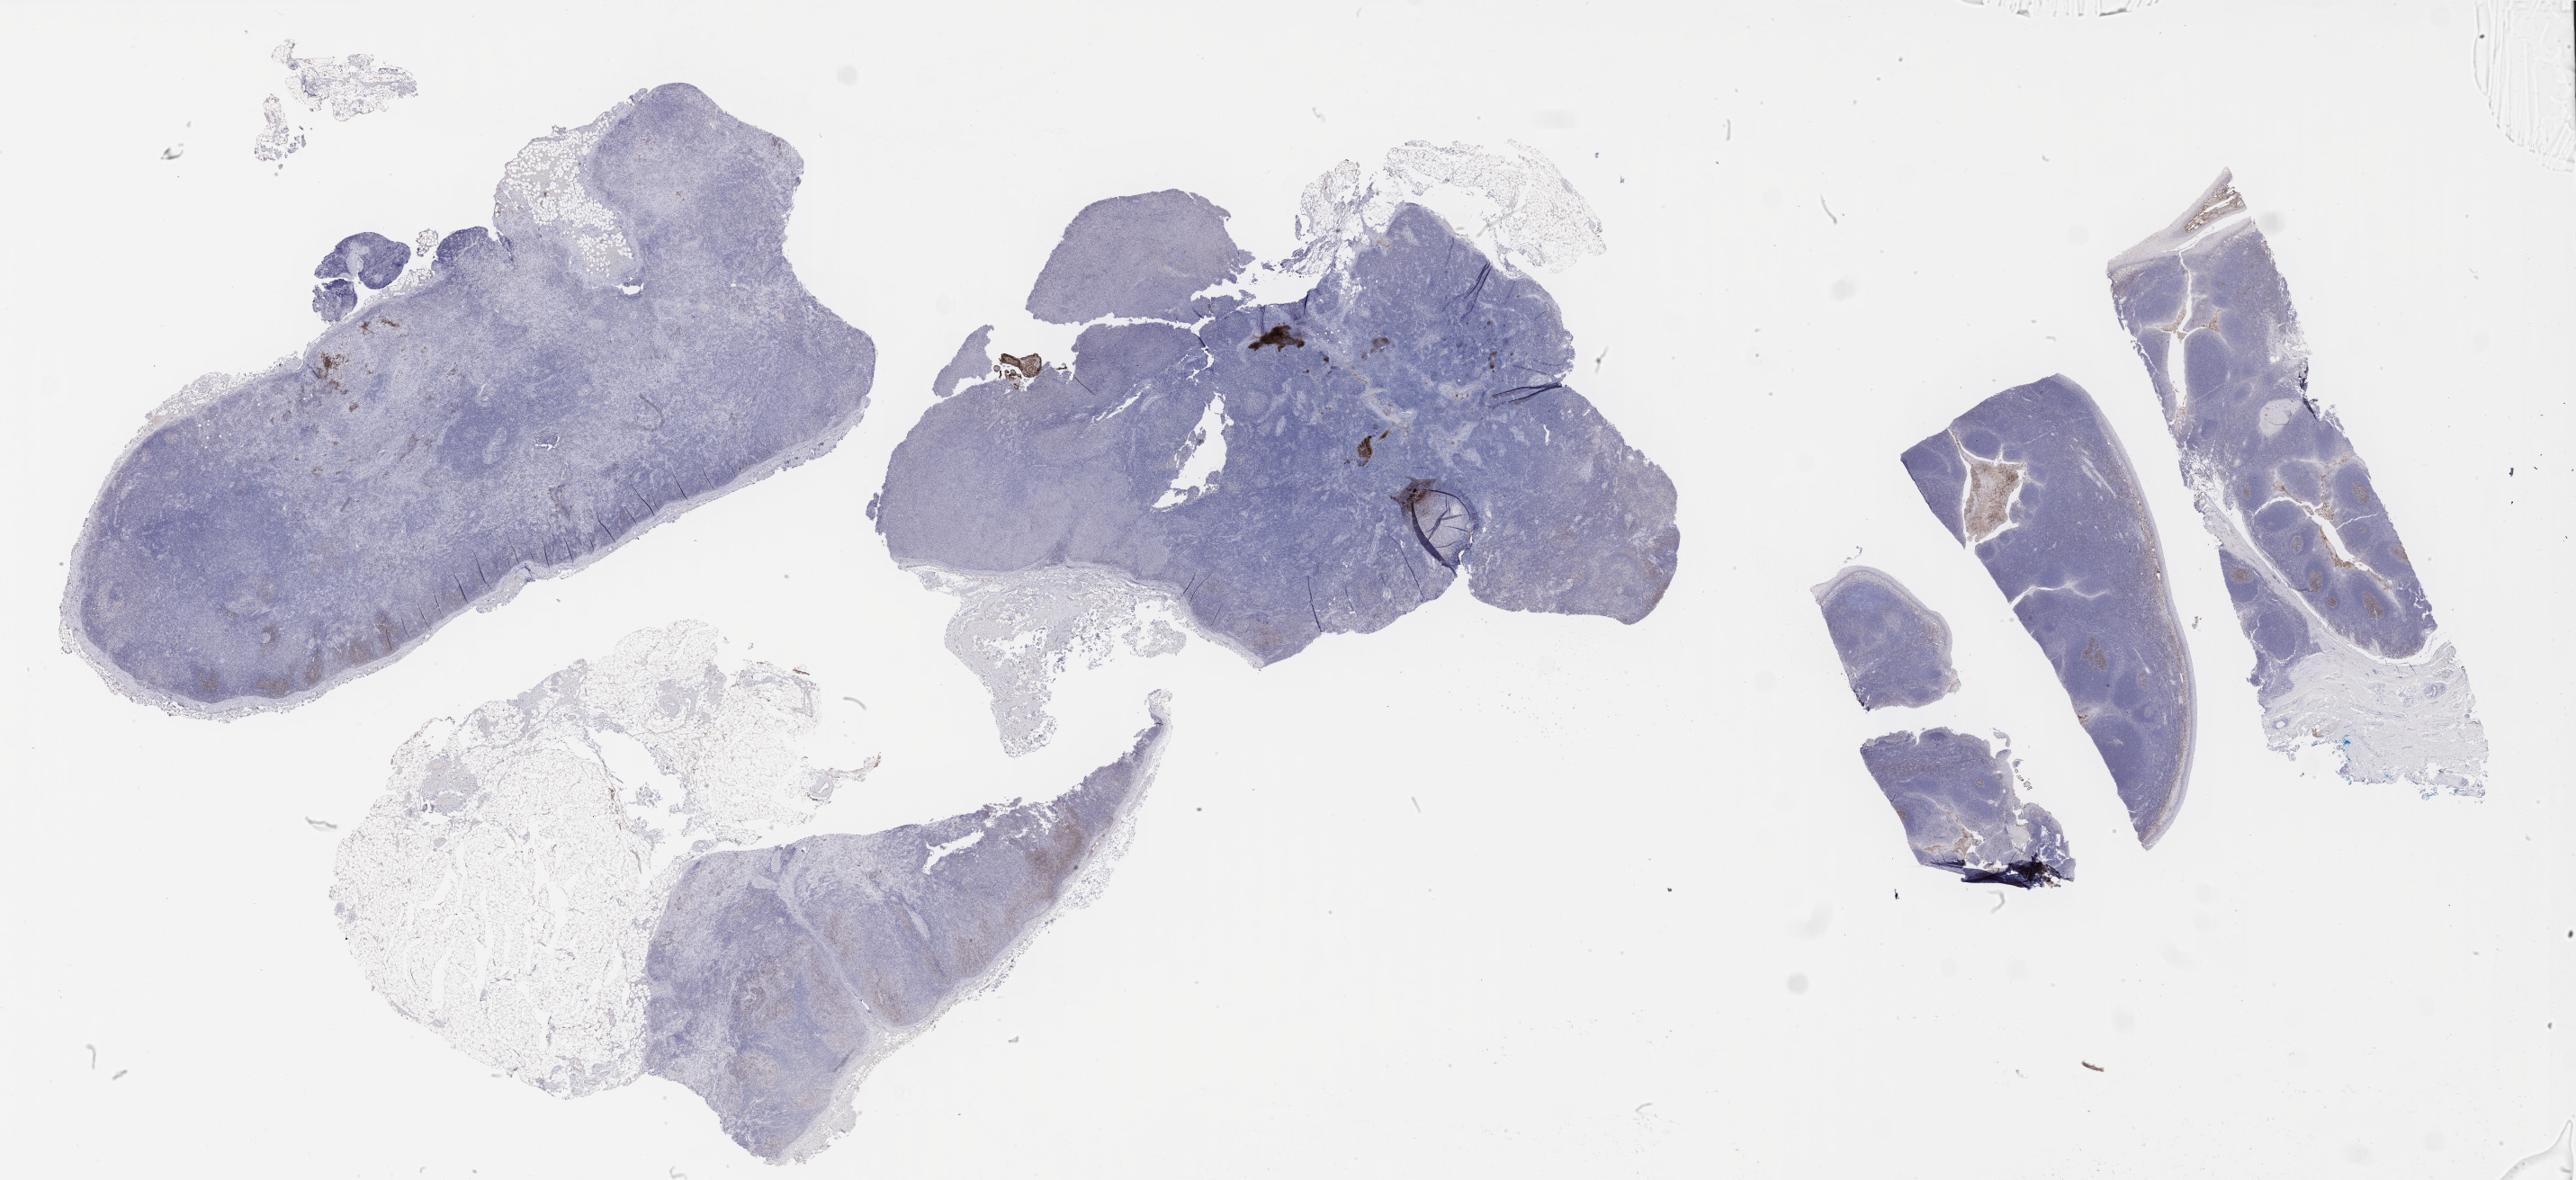
IHC for CD10, whole-slide image — shown as a low-resolution overview of the whole scanned area (about 46.3 x 21.2 mm); tumor tissue; anatomic site: lymph node. Patient: male, aged 56.
Diagnosis: Diffuse large B-cell lymphoma, NOS.